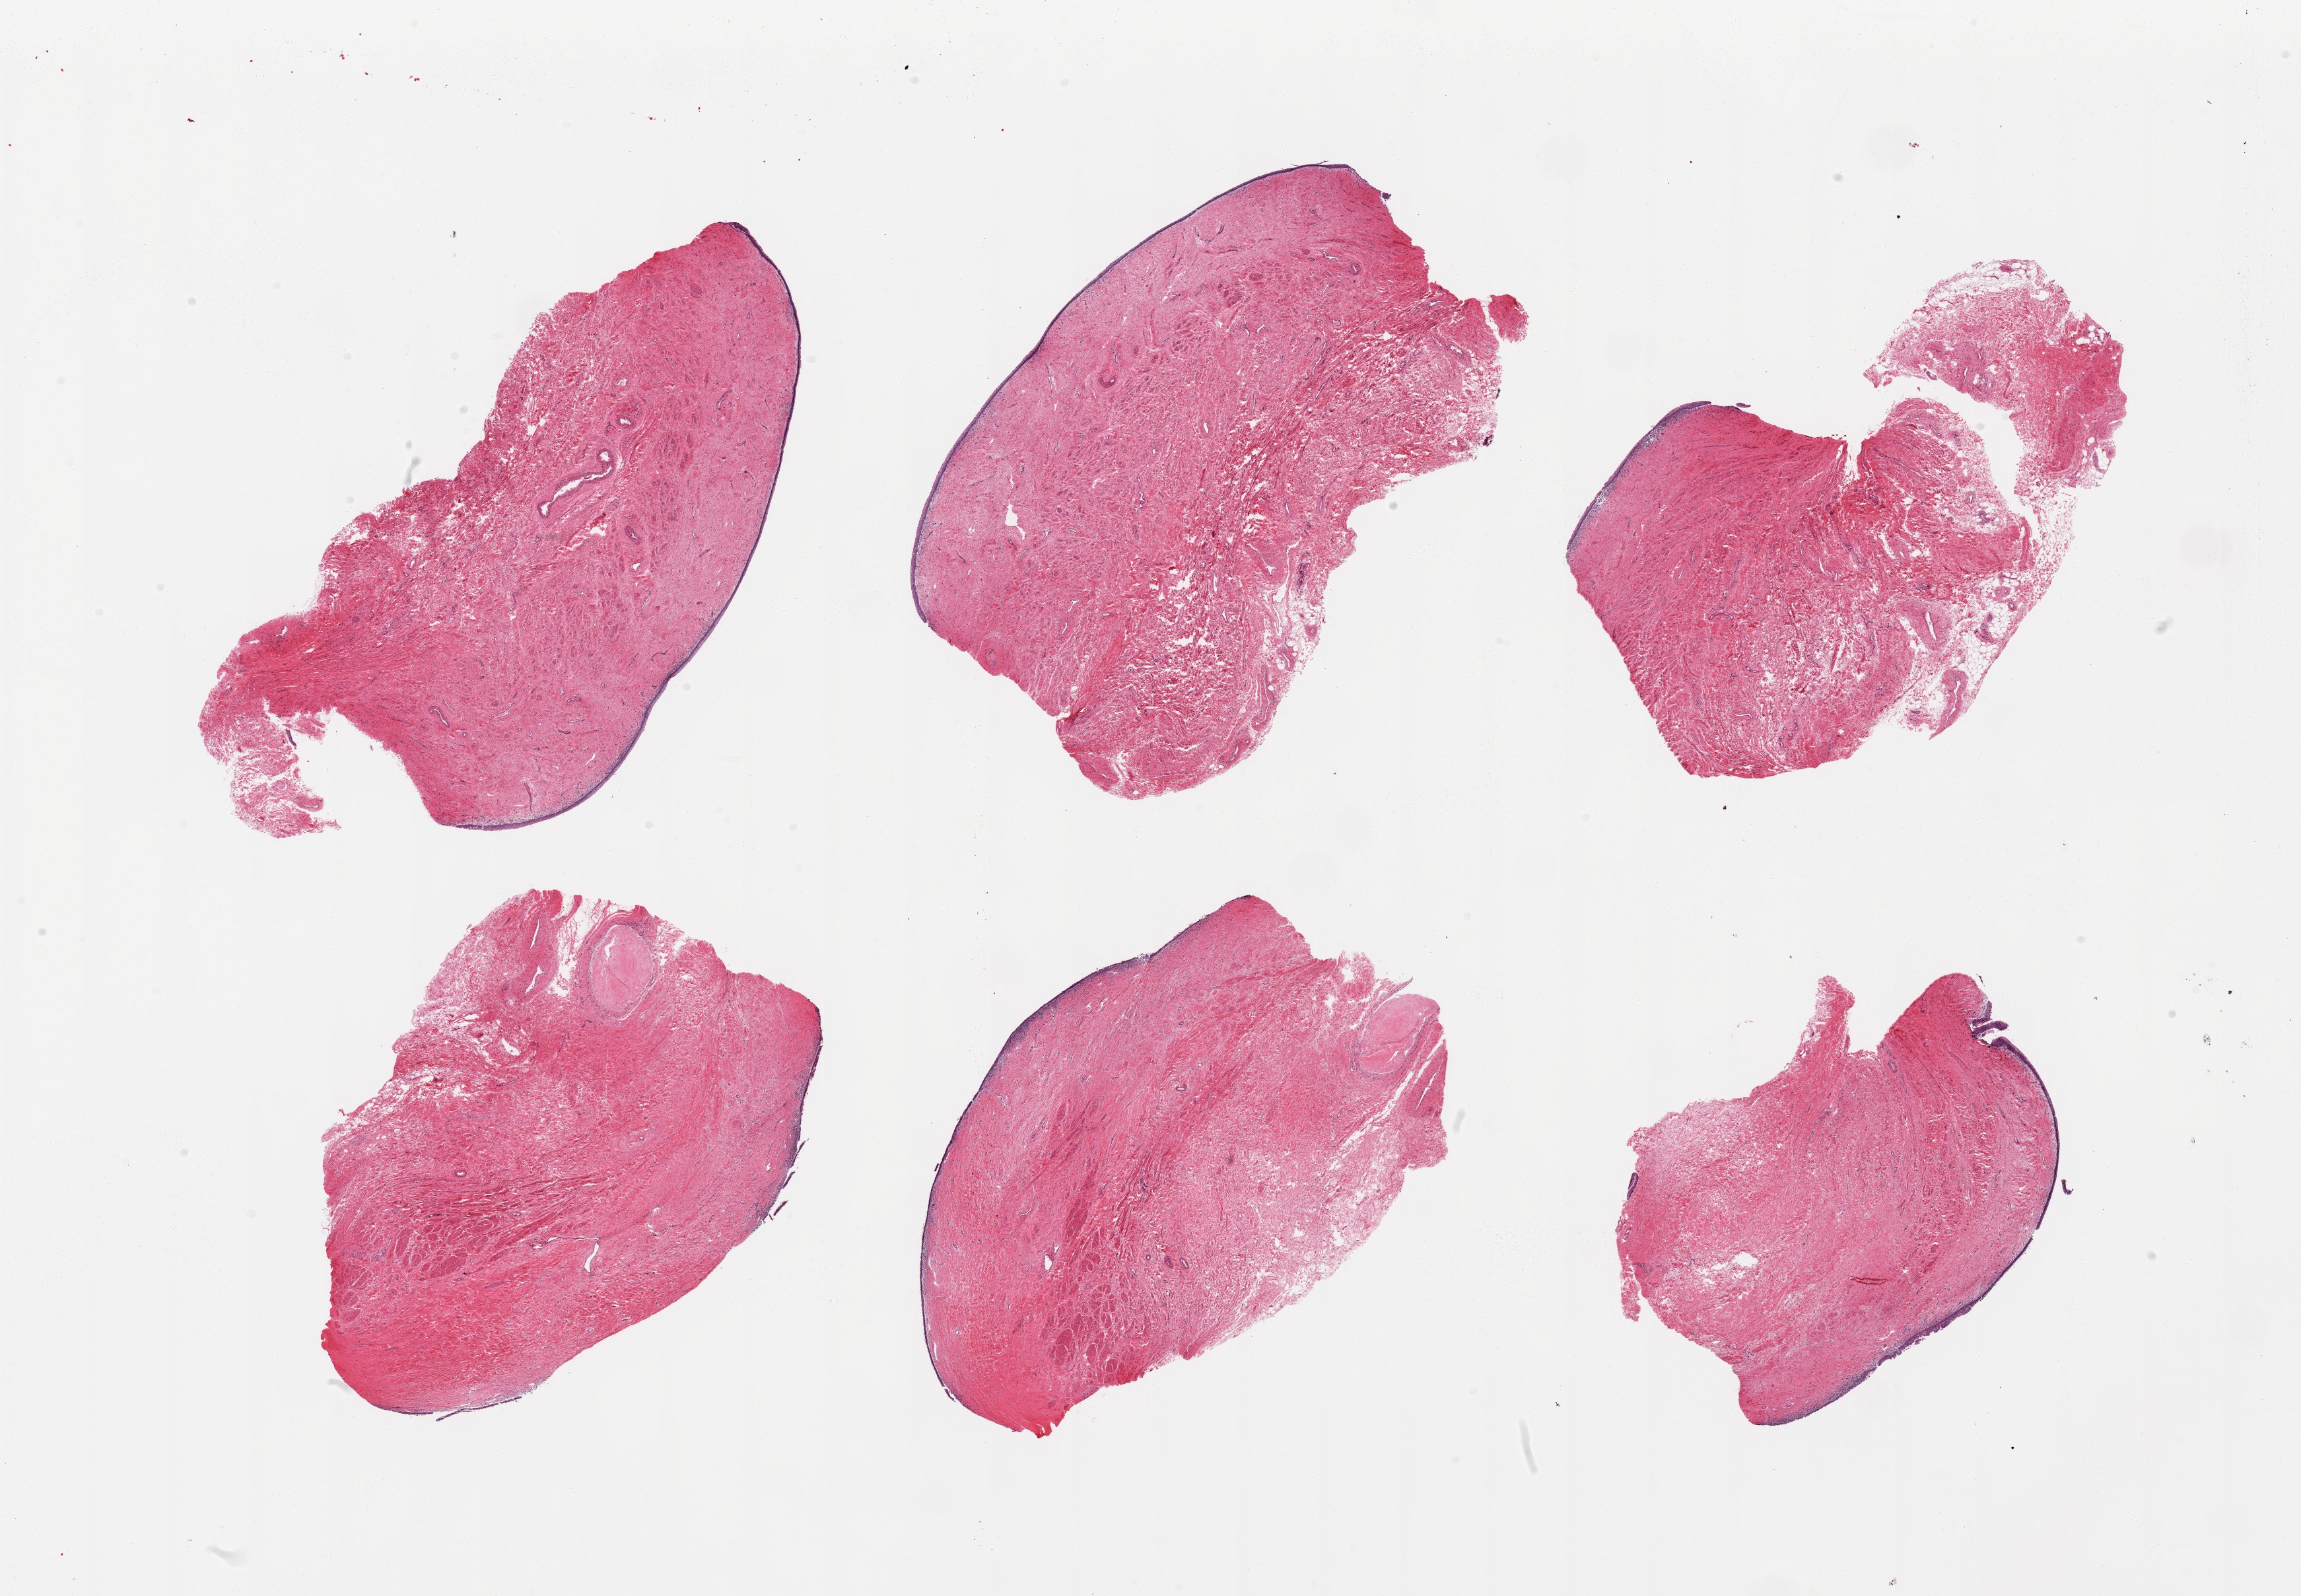
Digitized hematoxylin and eosin (H&E)-stained section, brightfield — whole scanned area (about 27.6 x 19.1 mm) shown as a low-resolution overview. PAXgene-fixed paraffin-embedded (PFPE) section. Section of vagina (target tissue). Donor tissue sample. Female donor.
Reviewer comment on this tissue sample: 6 pieces; squamous mucosa with mild, predominantly chronic, inflammation.